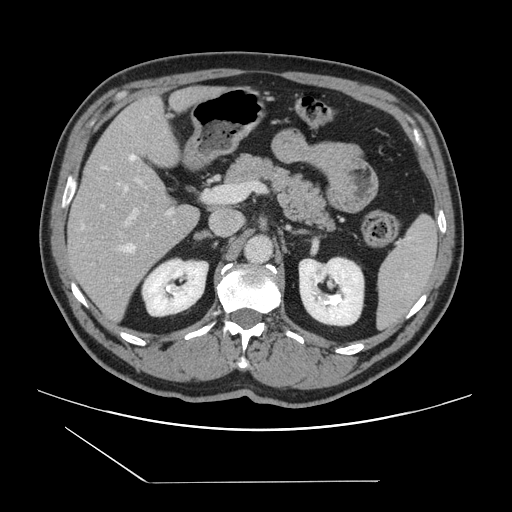
Contrast-enhanced abdominal CT, one axial slice. Position 78 of 157 along the scan axis. 120 kVp. Soft-tissue window (W 400 / L 40 HU). 2.5 mm slice thickness. 512 × 512 image matrix, field of view 407 × 407 mm. Male patient, age 61 years. Case-level facts recorded for this patient, not image findings: diagnosis: colorectal cancer liver metastases, imaged before liver resection; multiple liver metastases: yes; largest metastasis: 5.5 cm; disease in both lobes: yes.
Outlined on this slice (expert manual segmentation):
- hepatic veins: bounding box <106,155,136,252> (left, top, right, bottom; pixels)
- liver: <68,88,212,328>
- planned liver remnant (the part of the liver to remain after resection): <71,88,215,220>
- portal vein (with intrahepatic branches): <102,179,173,226>